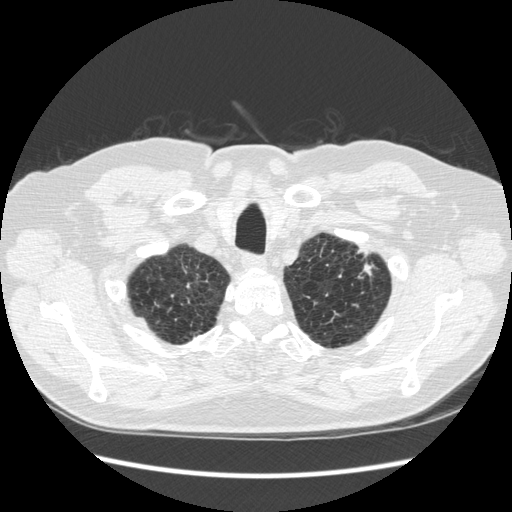
Low-dose screening chest CT, one axial slice; position 242 of 267 along the scan axis; 120 kVp; lung window (W 1500 / L -600 HU); 1.25 mm slice thickness; 512 × 512 image matrix, field of view 360 × 360 mm.
Structures marked on this image (expert manual segmentation):
- lesion 1 (tumor, upper lobe of left lung): box from (x=358, y=264) to (x=373, y=278) px